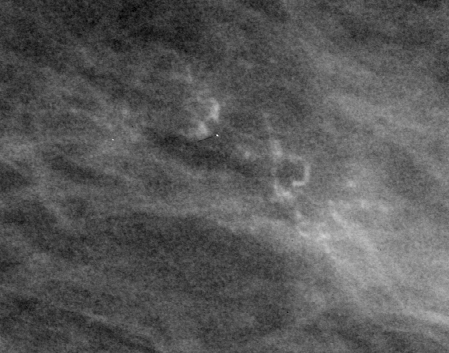
Crop from a digitized film mammogram around one marked abnormality, left breast, MLO view, BI-RADS breast density category 3 (scale 1–4).
- Finding: calcifications, morphology pleomorphic / fine linear branching, distribution clustered / linear; BI-RADS assessment category 5; subtlety rating 4 on a 1 (subtle) to 5 (obvious) scale; pathology result (as recorded, not read from the image): malignant.